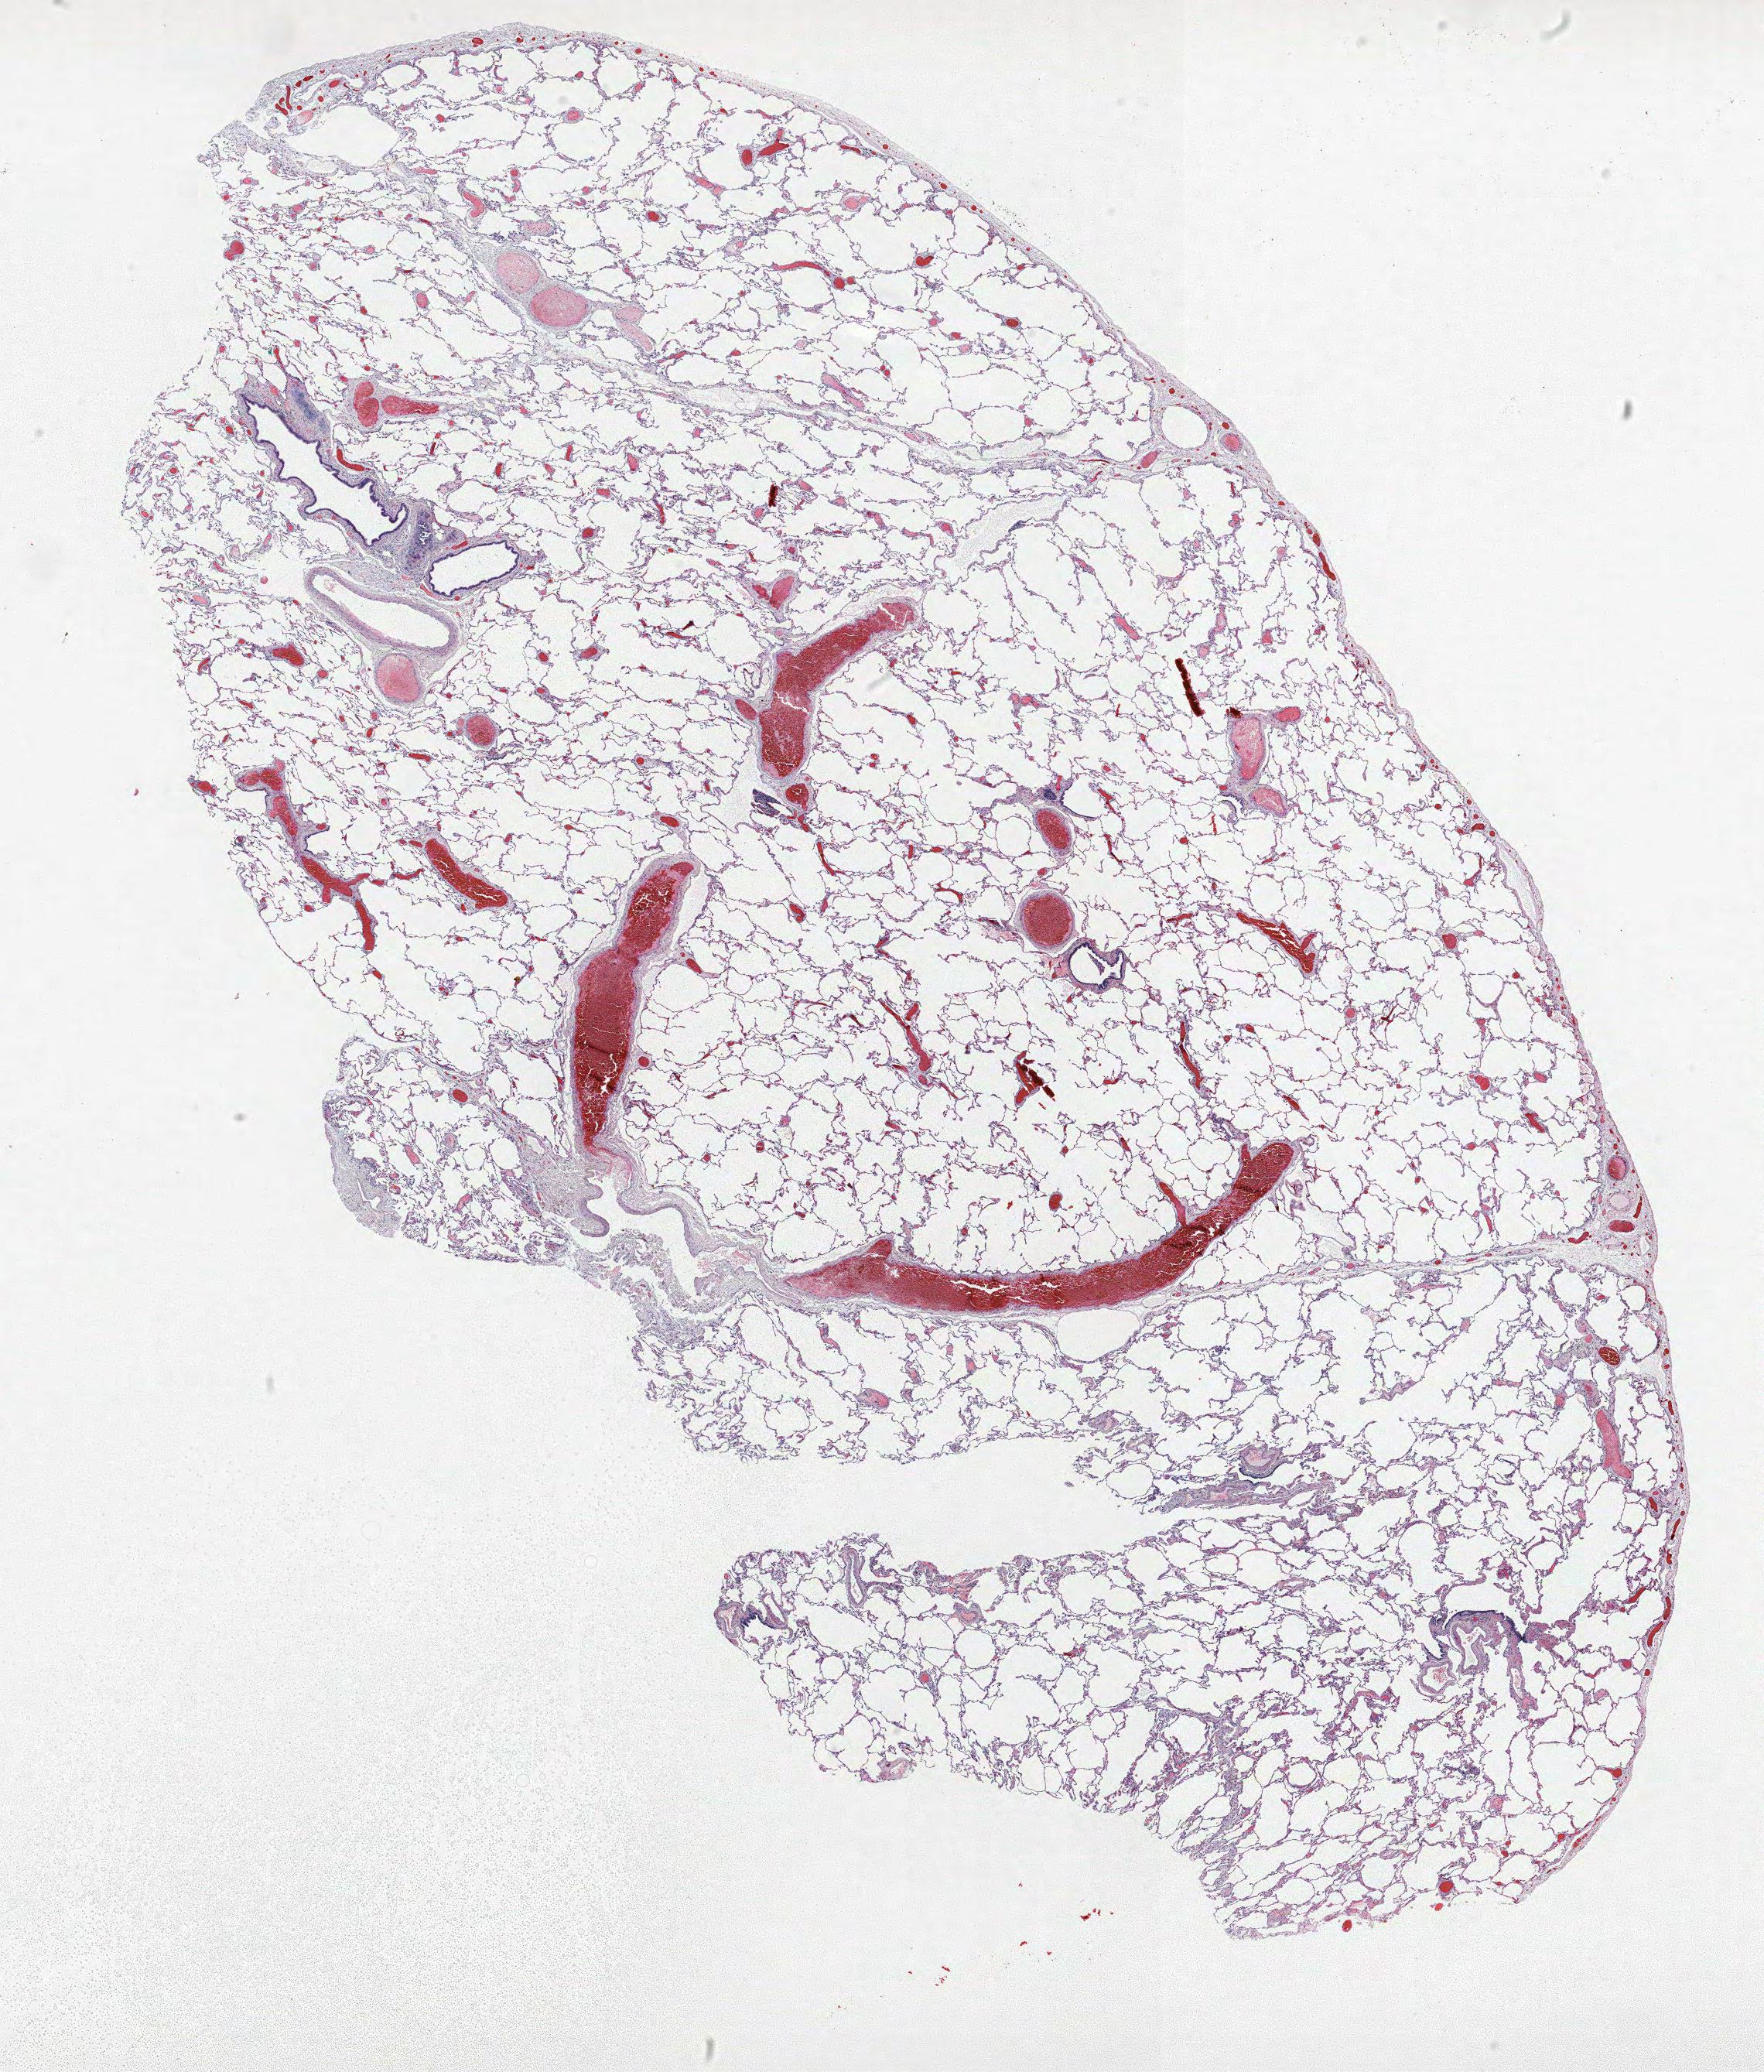
Whole-slide histology image, H&E-stained, low-resolution overview of the scanned area, about 18.2 x 21.4 mm (from a 40x scan). FFPE section. Lung tissue. Male, age 64 at enrolment. Former smoker at enrolment. Grade: poorly differentiated (G3).
Participant's lung-cancer diagnosis: Bronchiolo-alveolar adenocarcinoma, NOS (ICD-O-3 8250/3). Primary tumour location (clinical record): right upper lobe. Stage (AJCC 6th edition): IA. Tumour size (pathology): 5 mm. Note: participant had 2 primary lung cancers recorded; fields above describe the first.